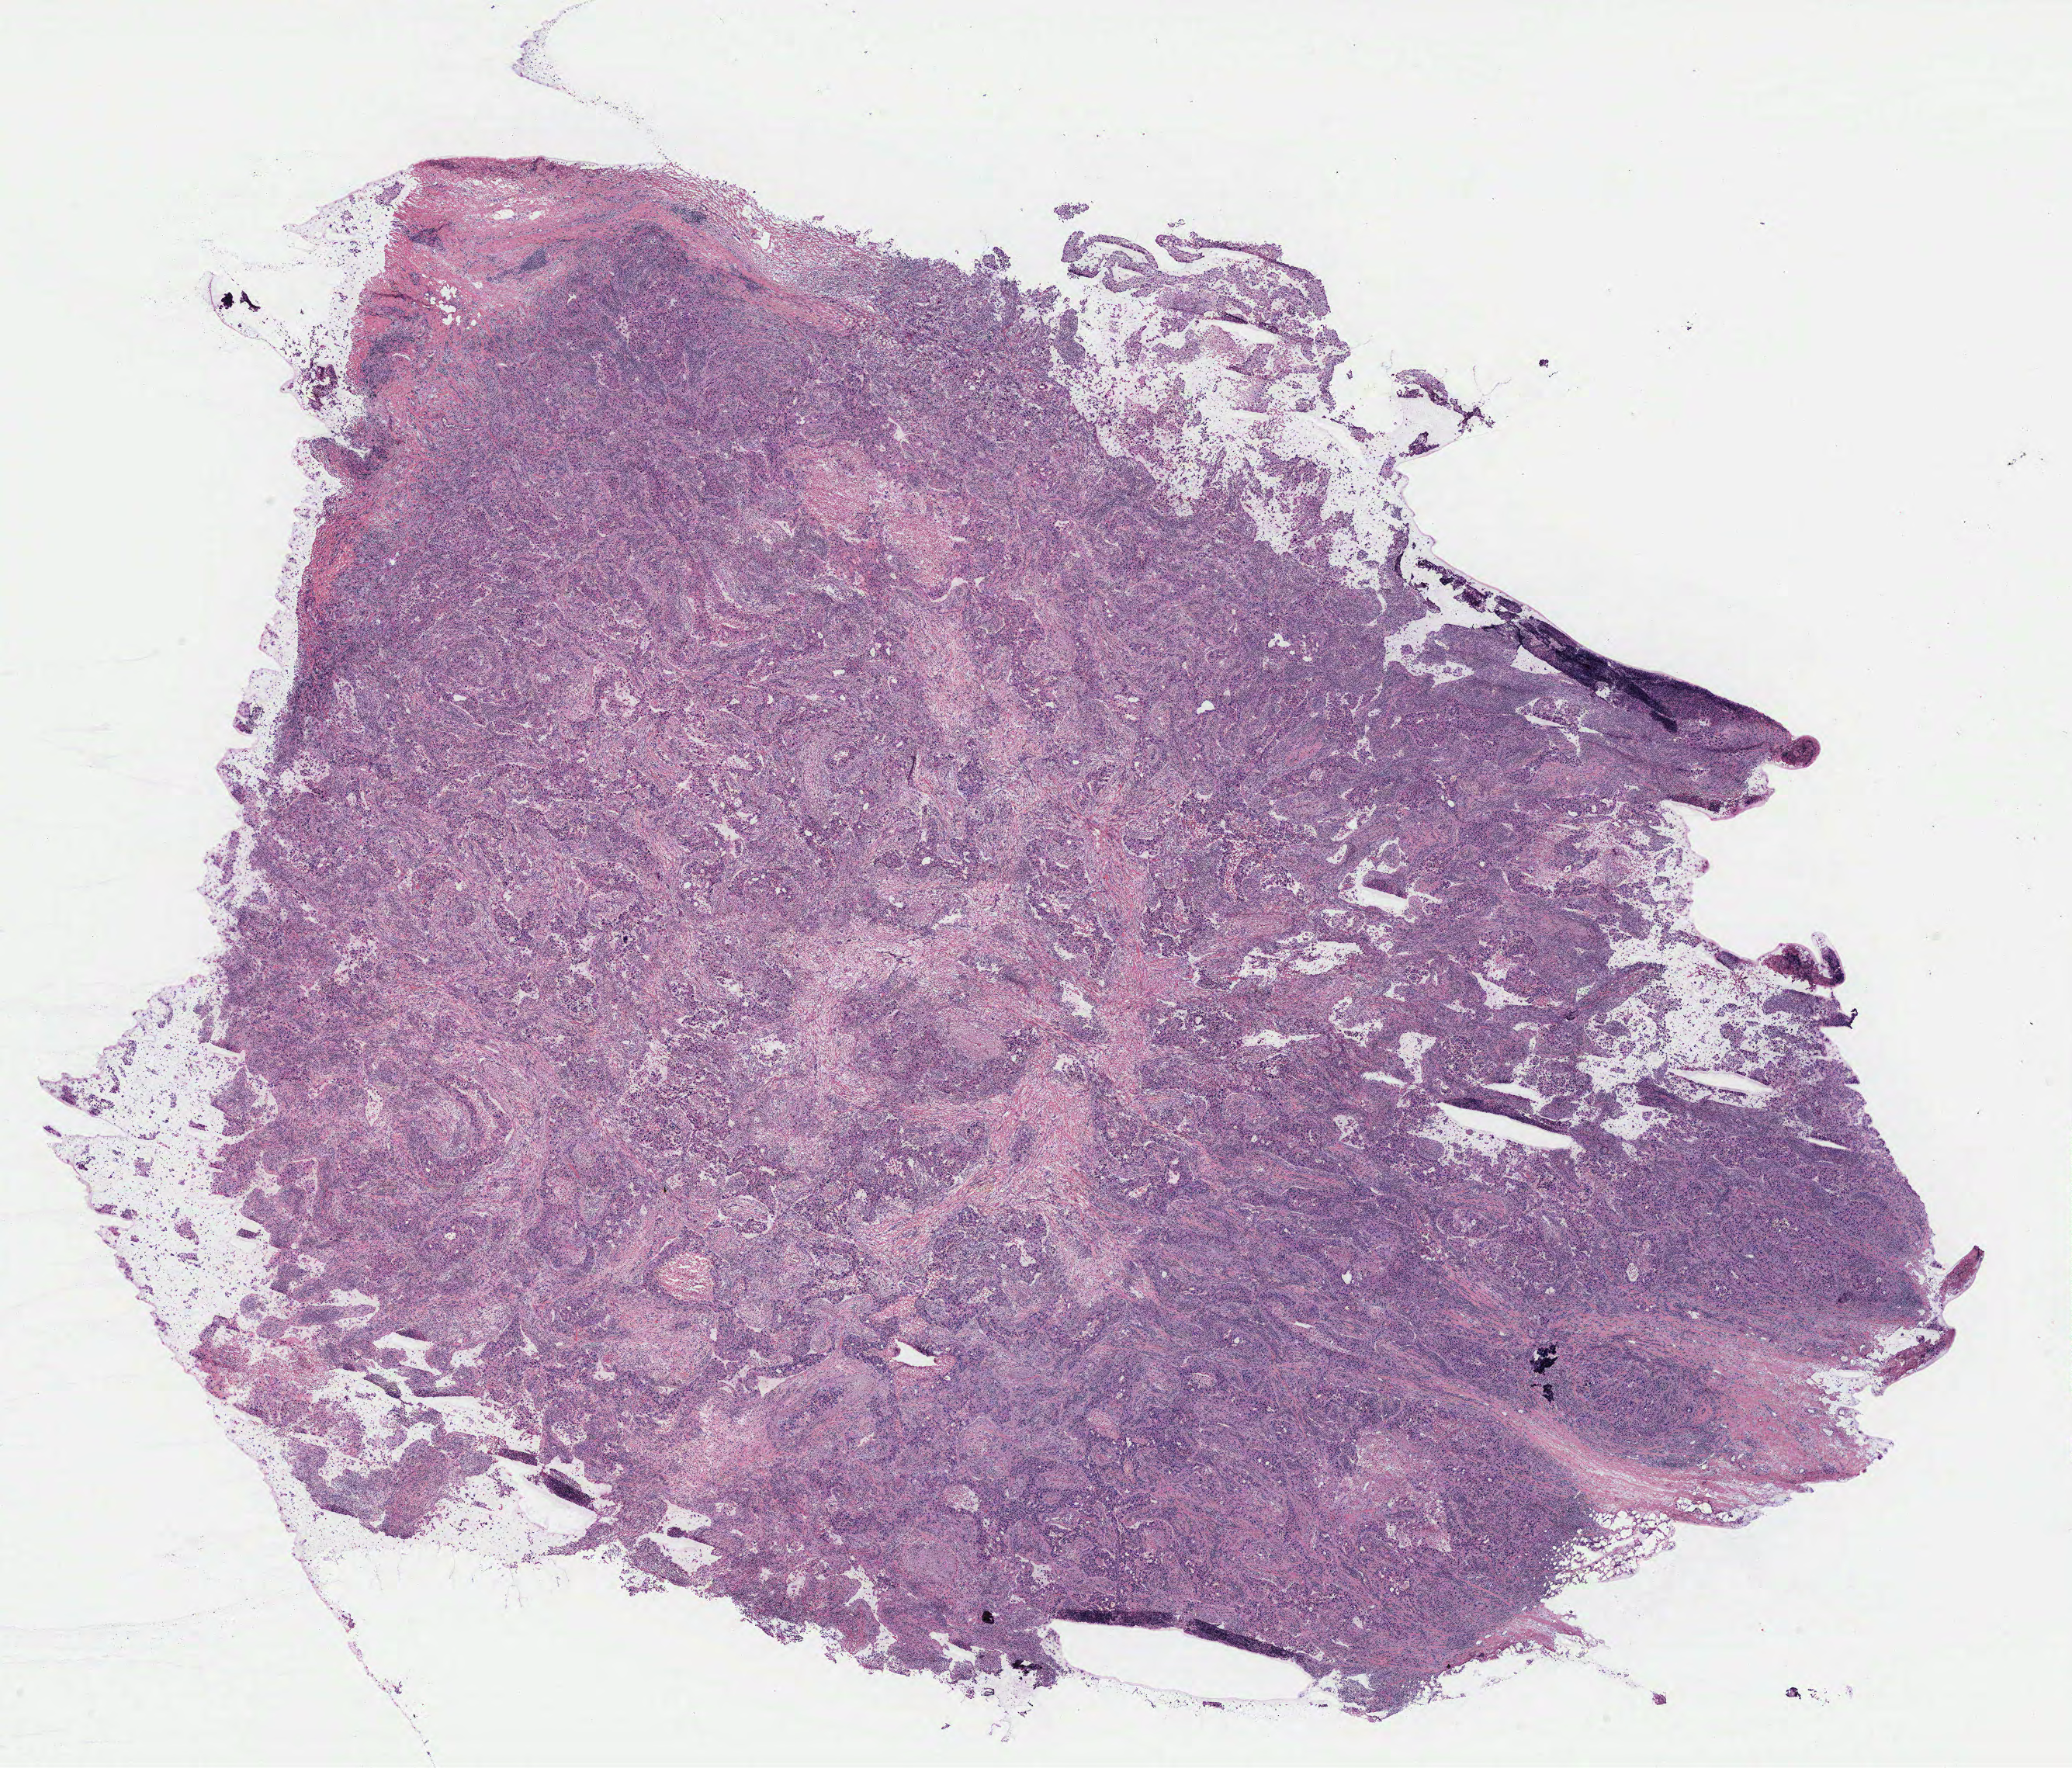
Digitized H&E-stained tissue section (whole slide), low-resolution overview of the scanned area, about 21.4 x 18.2 mm (from a 40x scan). Breast, tissue type not recorded. Female, 74 y/o.
Patient diagnosis: Infiltrating duct carcinoma, NOS.